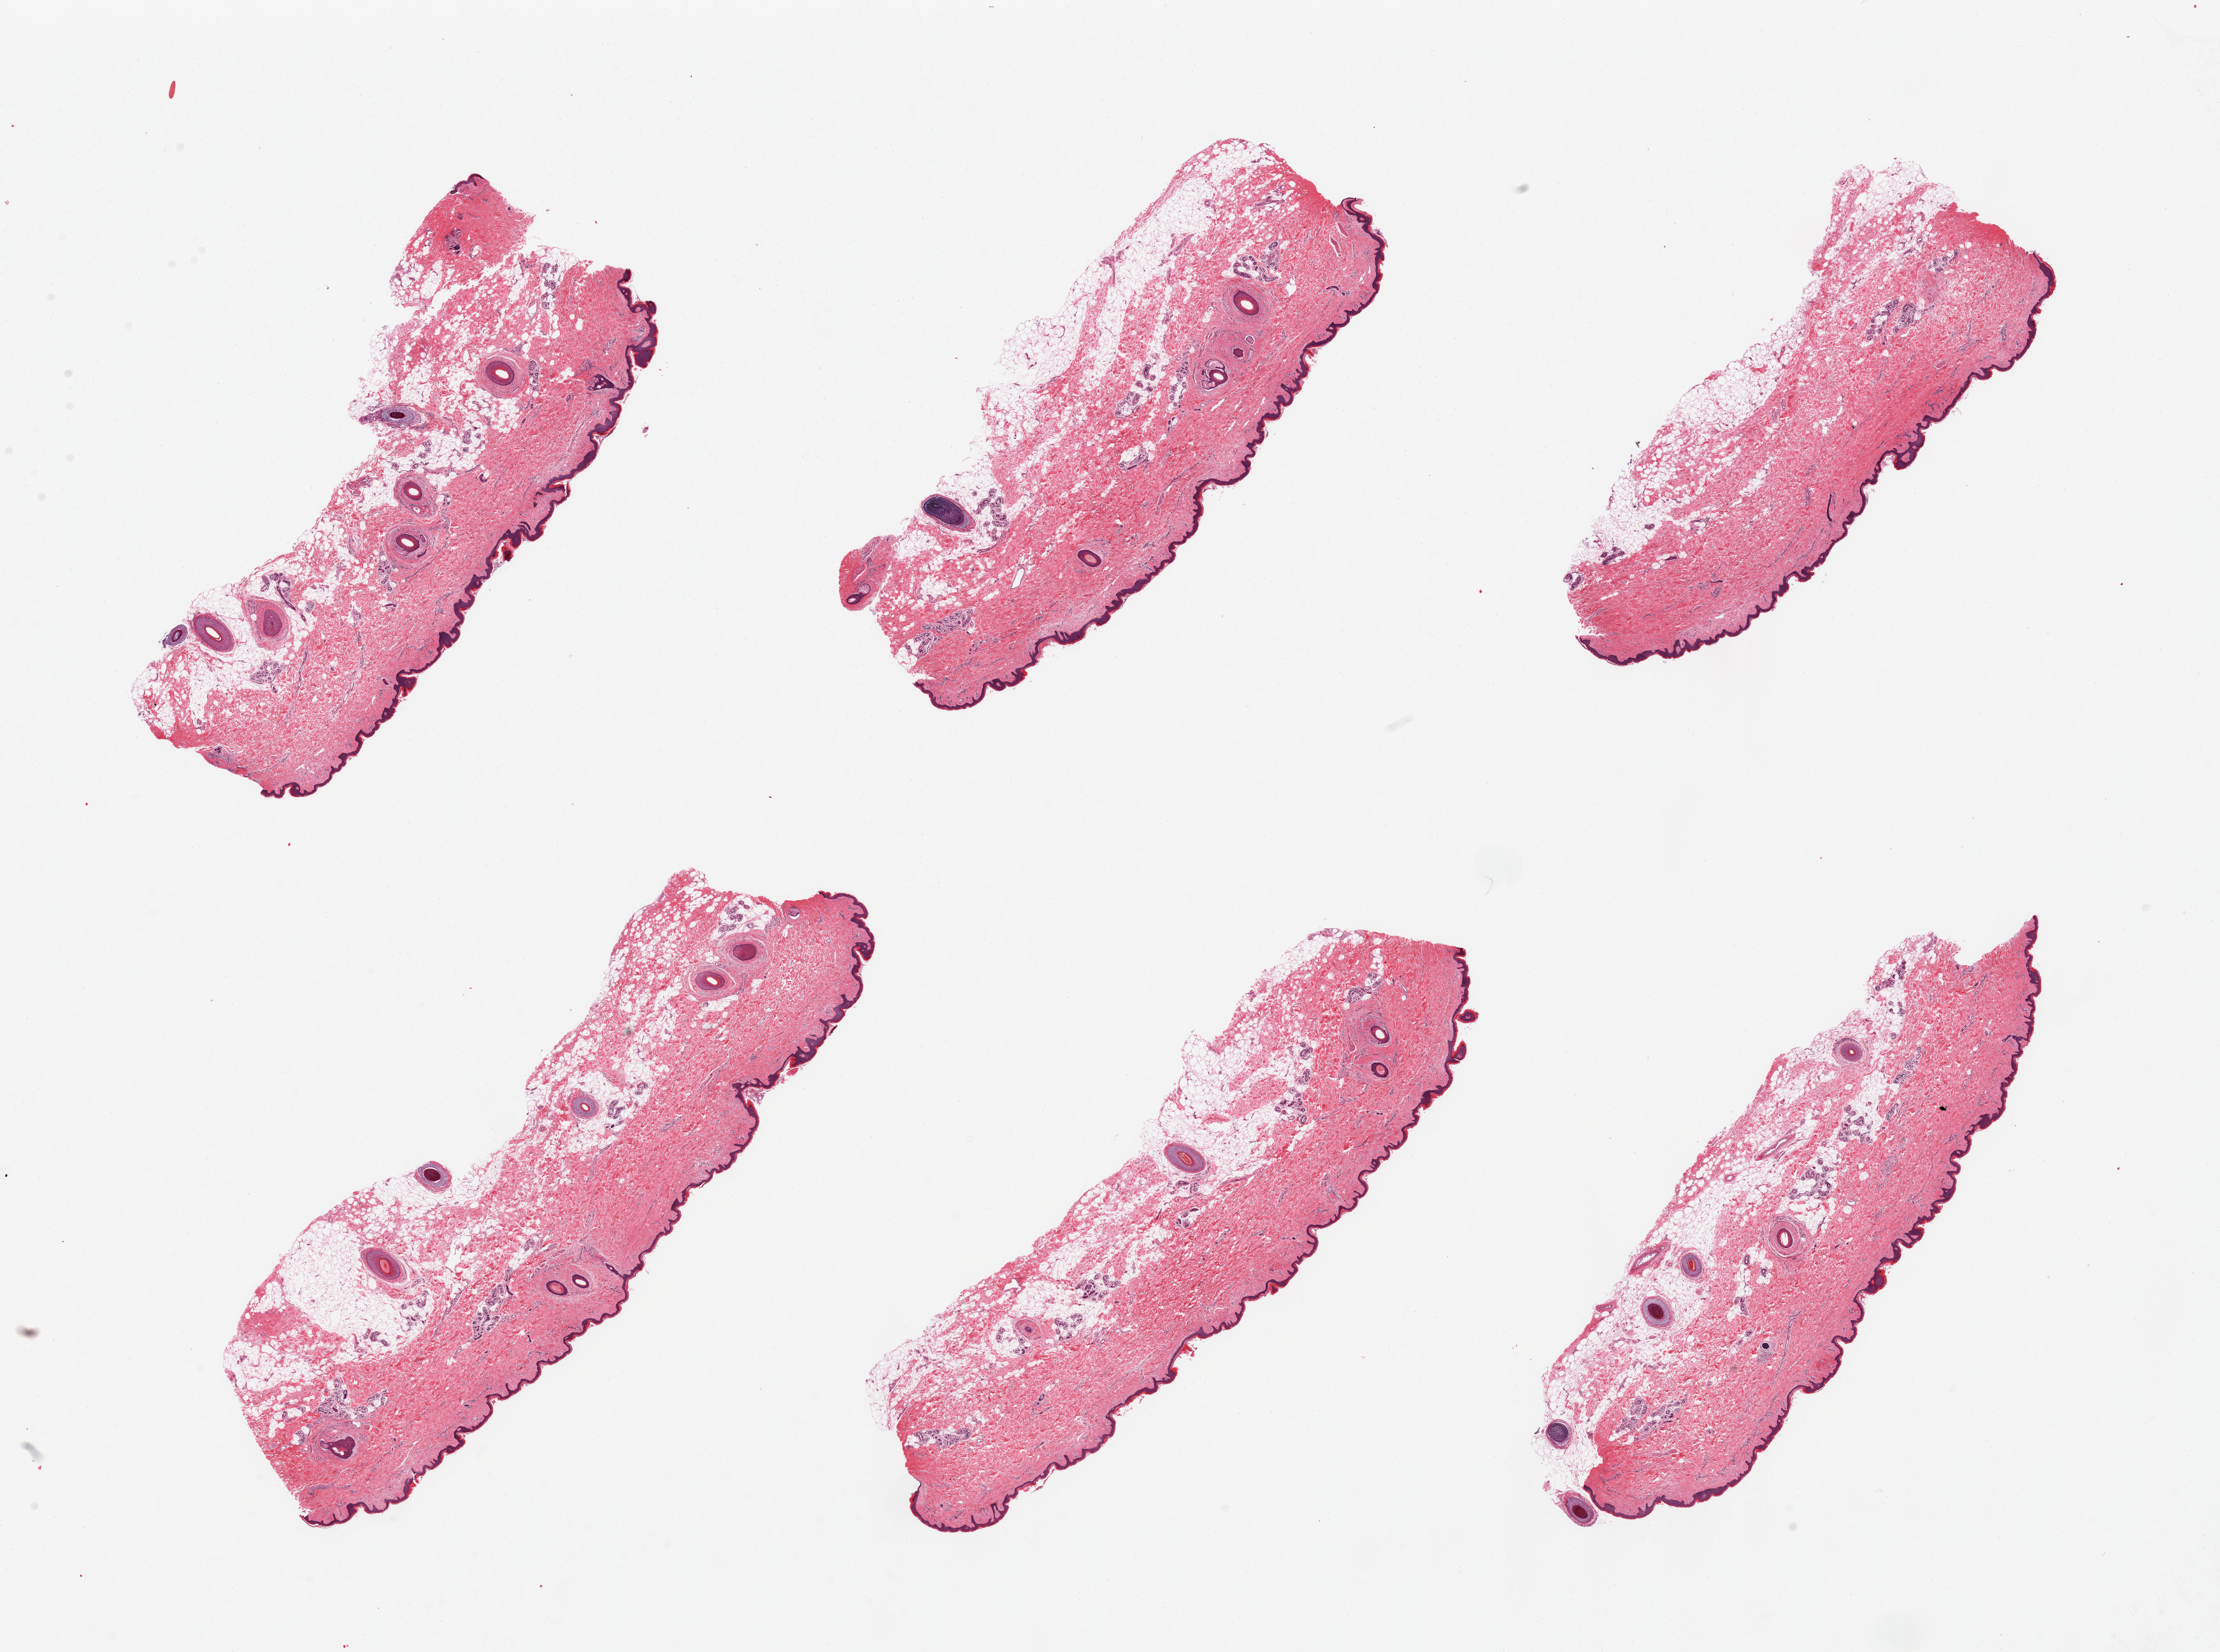
Whole-slide image, H&E stain, brightfield, whole scanned area (about 27.6 x 20.5 mm) shown as a low-resolution overview; PAXgene-fixed, paraffin-embedded tissue; sampled site (target tissue): skin of suprapubic region; donor tissue sample. Donor: male.
Pathologist's review note for this sample: 6 pieces, trace adherent dermal fat. Squamous epithelium averages ~50 microns.